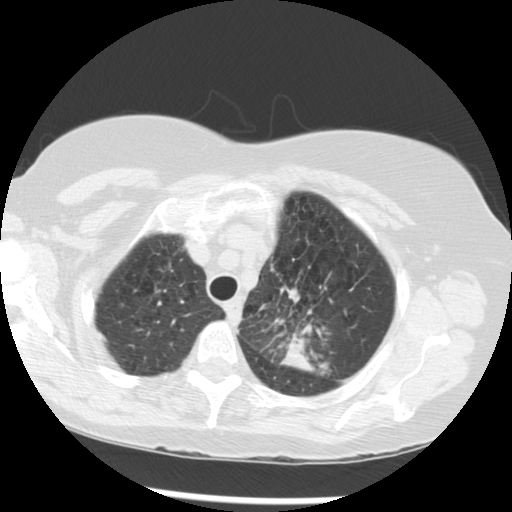
Low-dose screening chest CT, one axial slice. Position 233 of 283 along the scan axis. 120 kVp. Lung window (W 1500 / L -600 HU). 2.5 mm slice thickness. 512 × 512 image matrix, field of view 330 × 330 mm.
Annotated regions visible in this slice (outlined manually by an expert reader):
- lesion 1 (tumor, upper lobe of left lung): bounding box (x1, y1, x2, y2) in pixels: (279, 288, 318, 375)